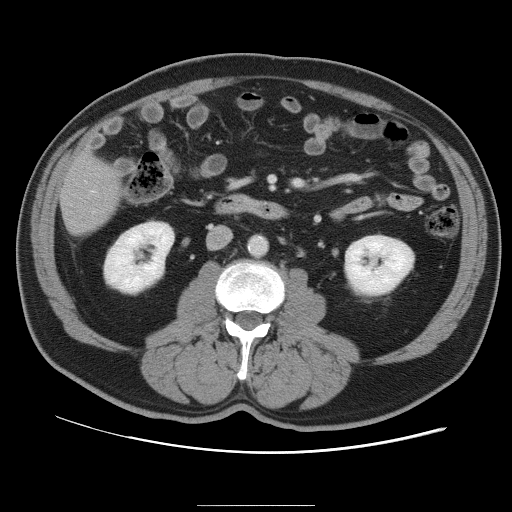
Contrast-enhanced abdominal CT, one axial slice. Position 26 of 105 along the scan axis. 120 kVp. Intravenous contrast given. Soft-tissue window (W 400 / L 40 HU). 512 × 512 image matrix. Male patient, age 64 years. From the clinical record (not read from this slice): diagnosis: colorectal cancer liver metastases, imaged before liver resection; multiple liver metastases: yes; largest metastasis: 3 cm.
Outlined on this slice (manually delineated by an expert):
- hepatic veins: bounding box <93,191,96,193> (left, top, right, bottom; pixels)
- liver: <62,159,119,234>
- planned liver remnant (the part of the liver to remain after resection): <63,159,119,228>